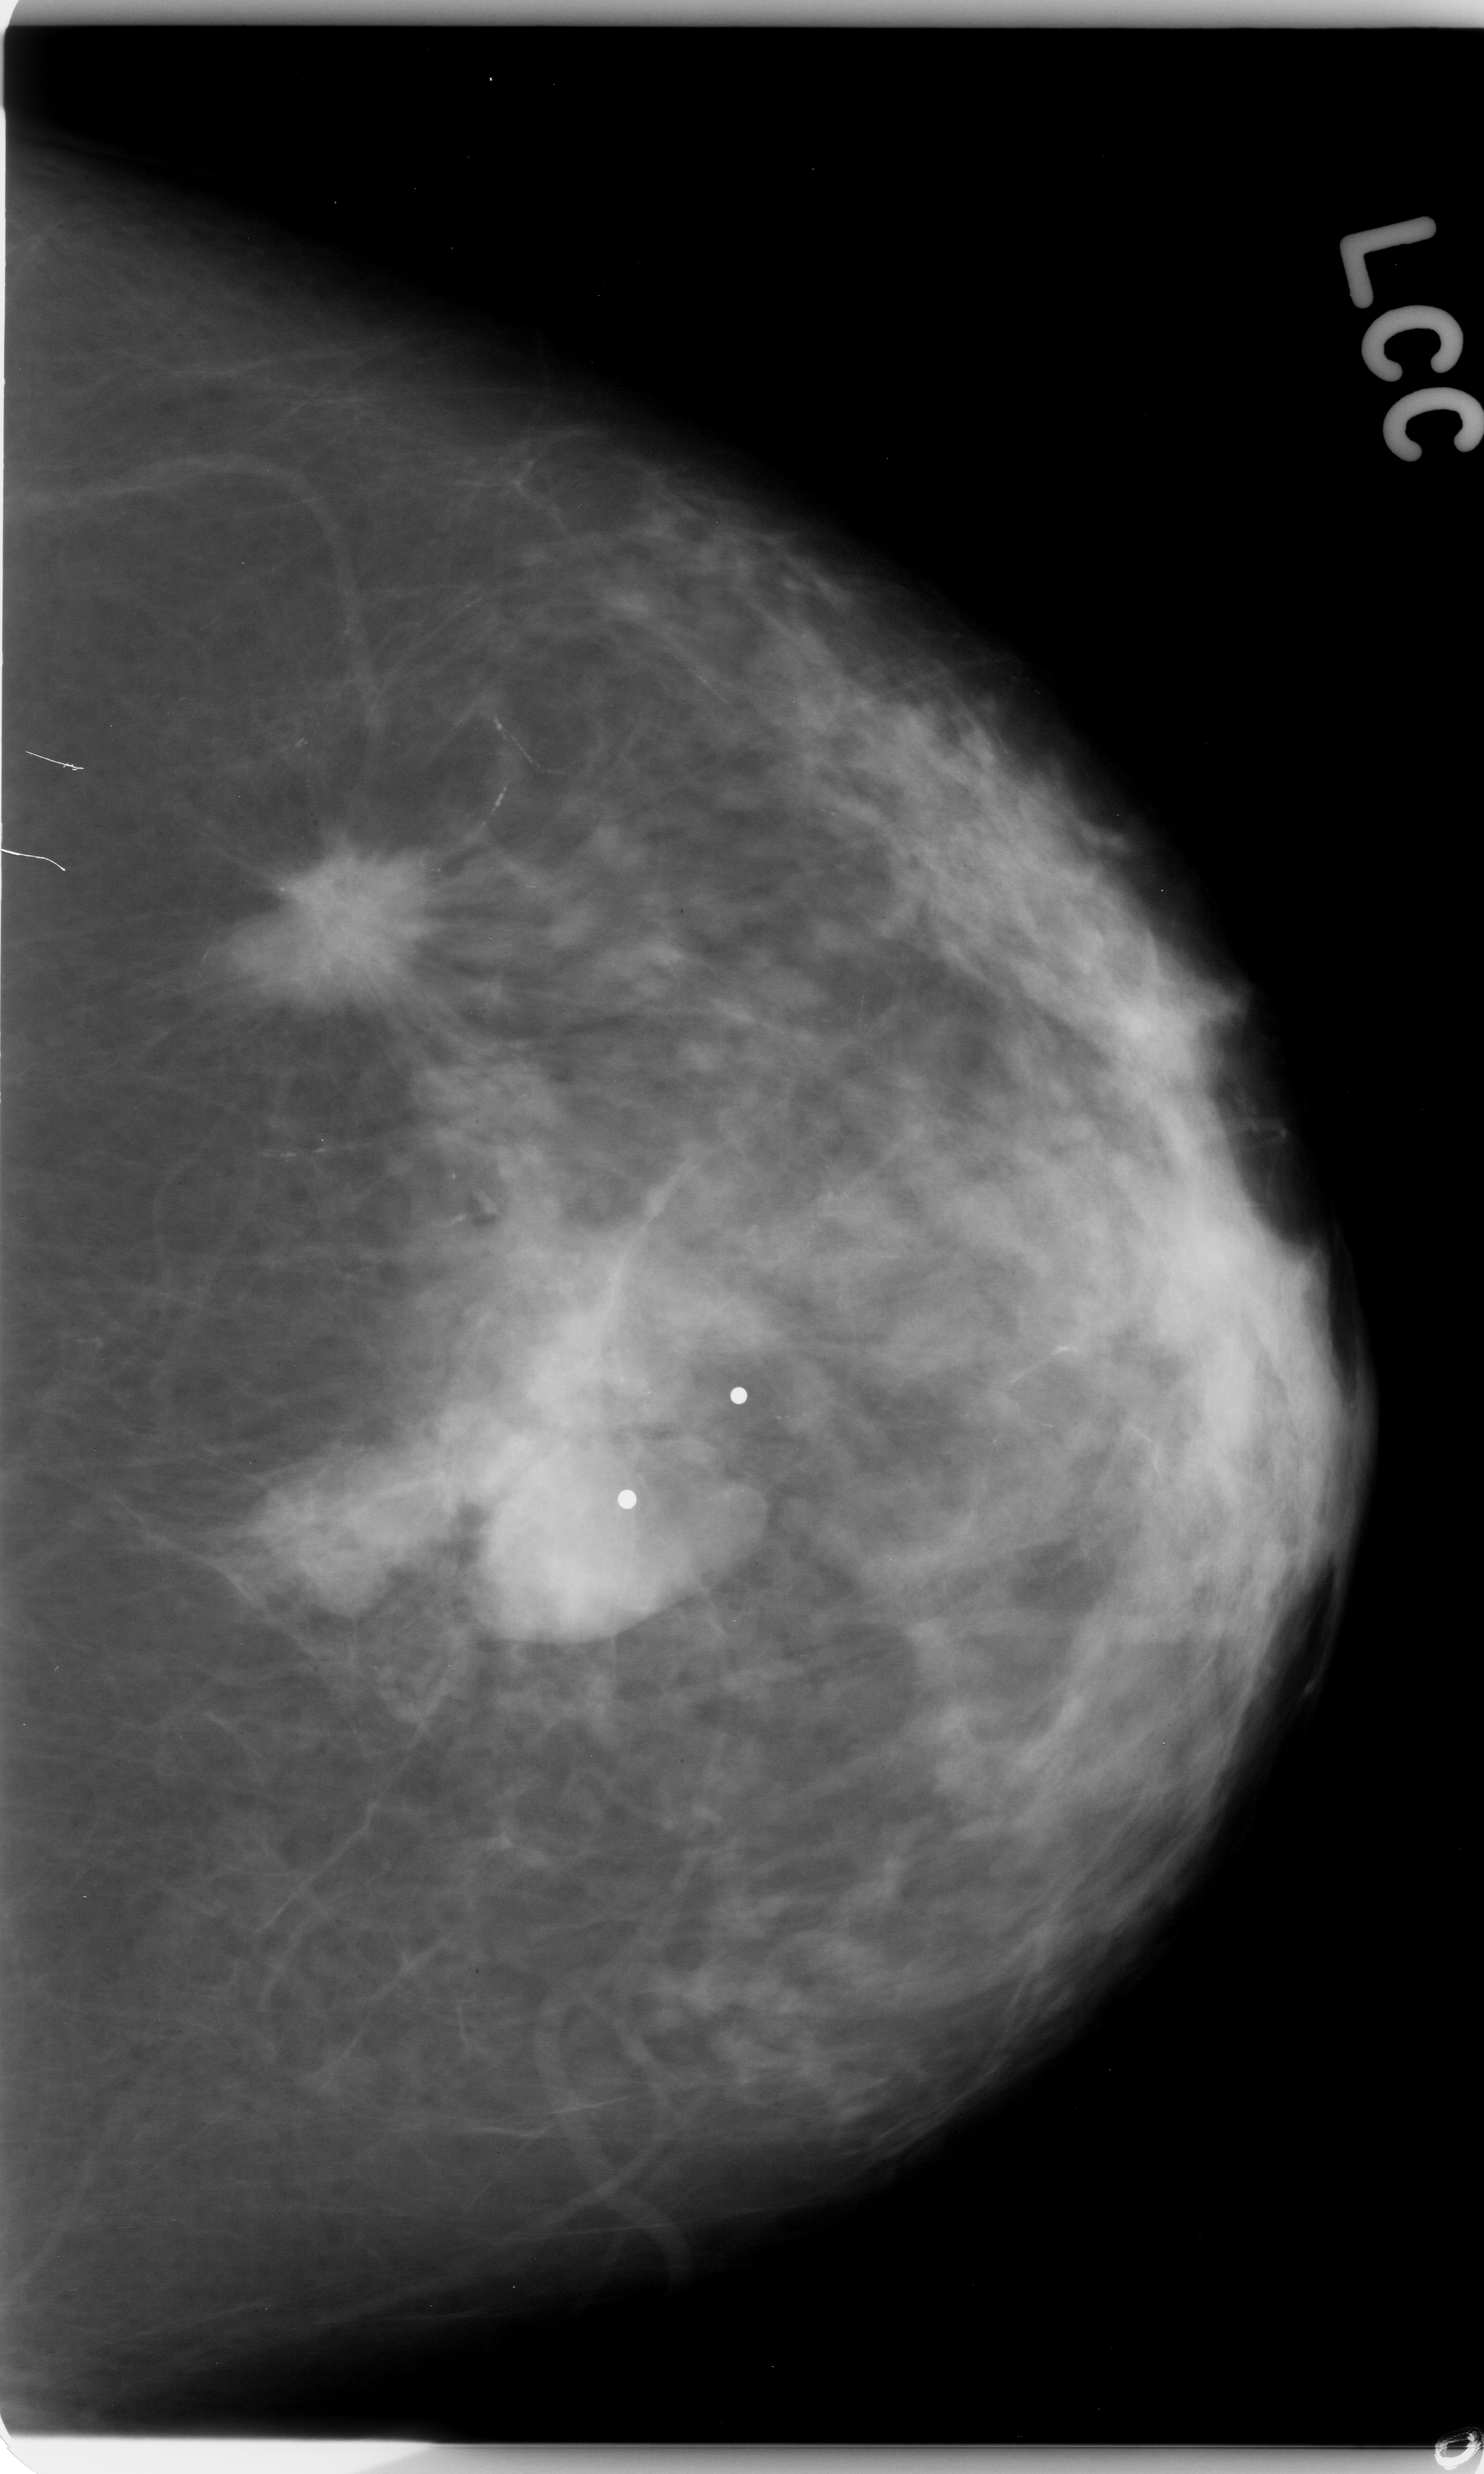
Scanned film-screen mammogram, left breast, craniocaudal (CC) view, breast composition: scattered fibroglandular densities (BI-RADS density category 2 of 4).
Marked findings (only marked abnormalities are described; nothing is implied about the rest of the image): mass, shape irregular, margins spiculated; BI-RADS assessment category 5; subtlety rating 5 on a 1 (subtle) to 5 (obvious) scale; pathology result (as recorded, not read from the image): malignant.